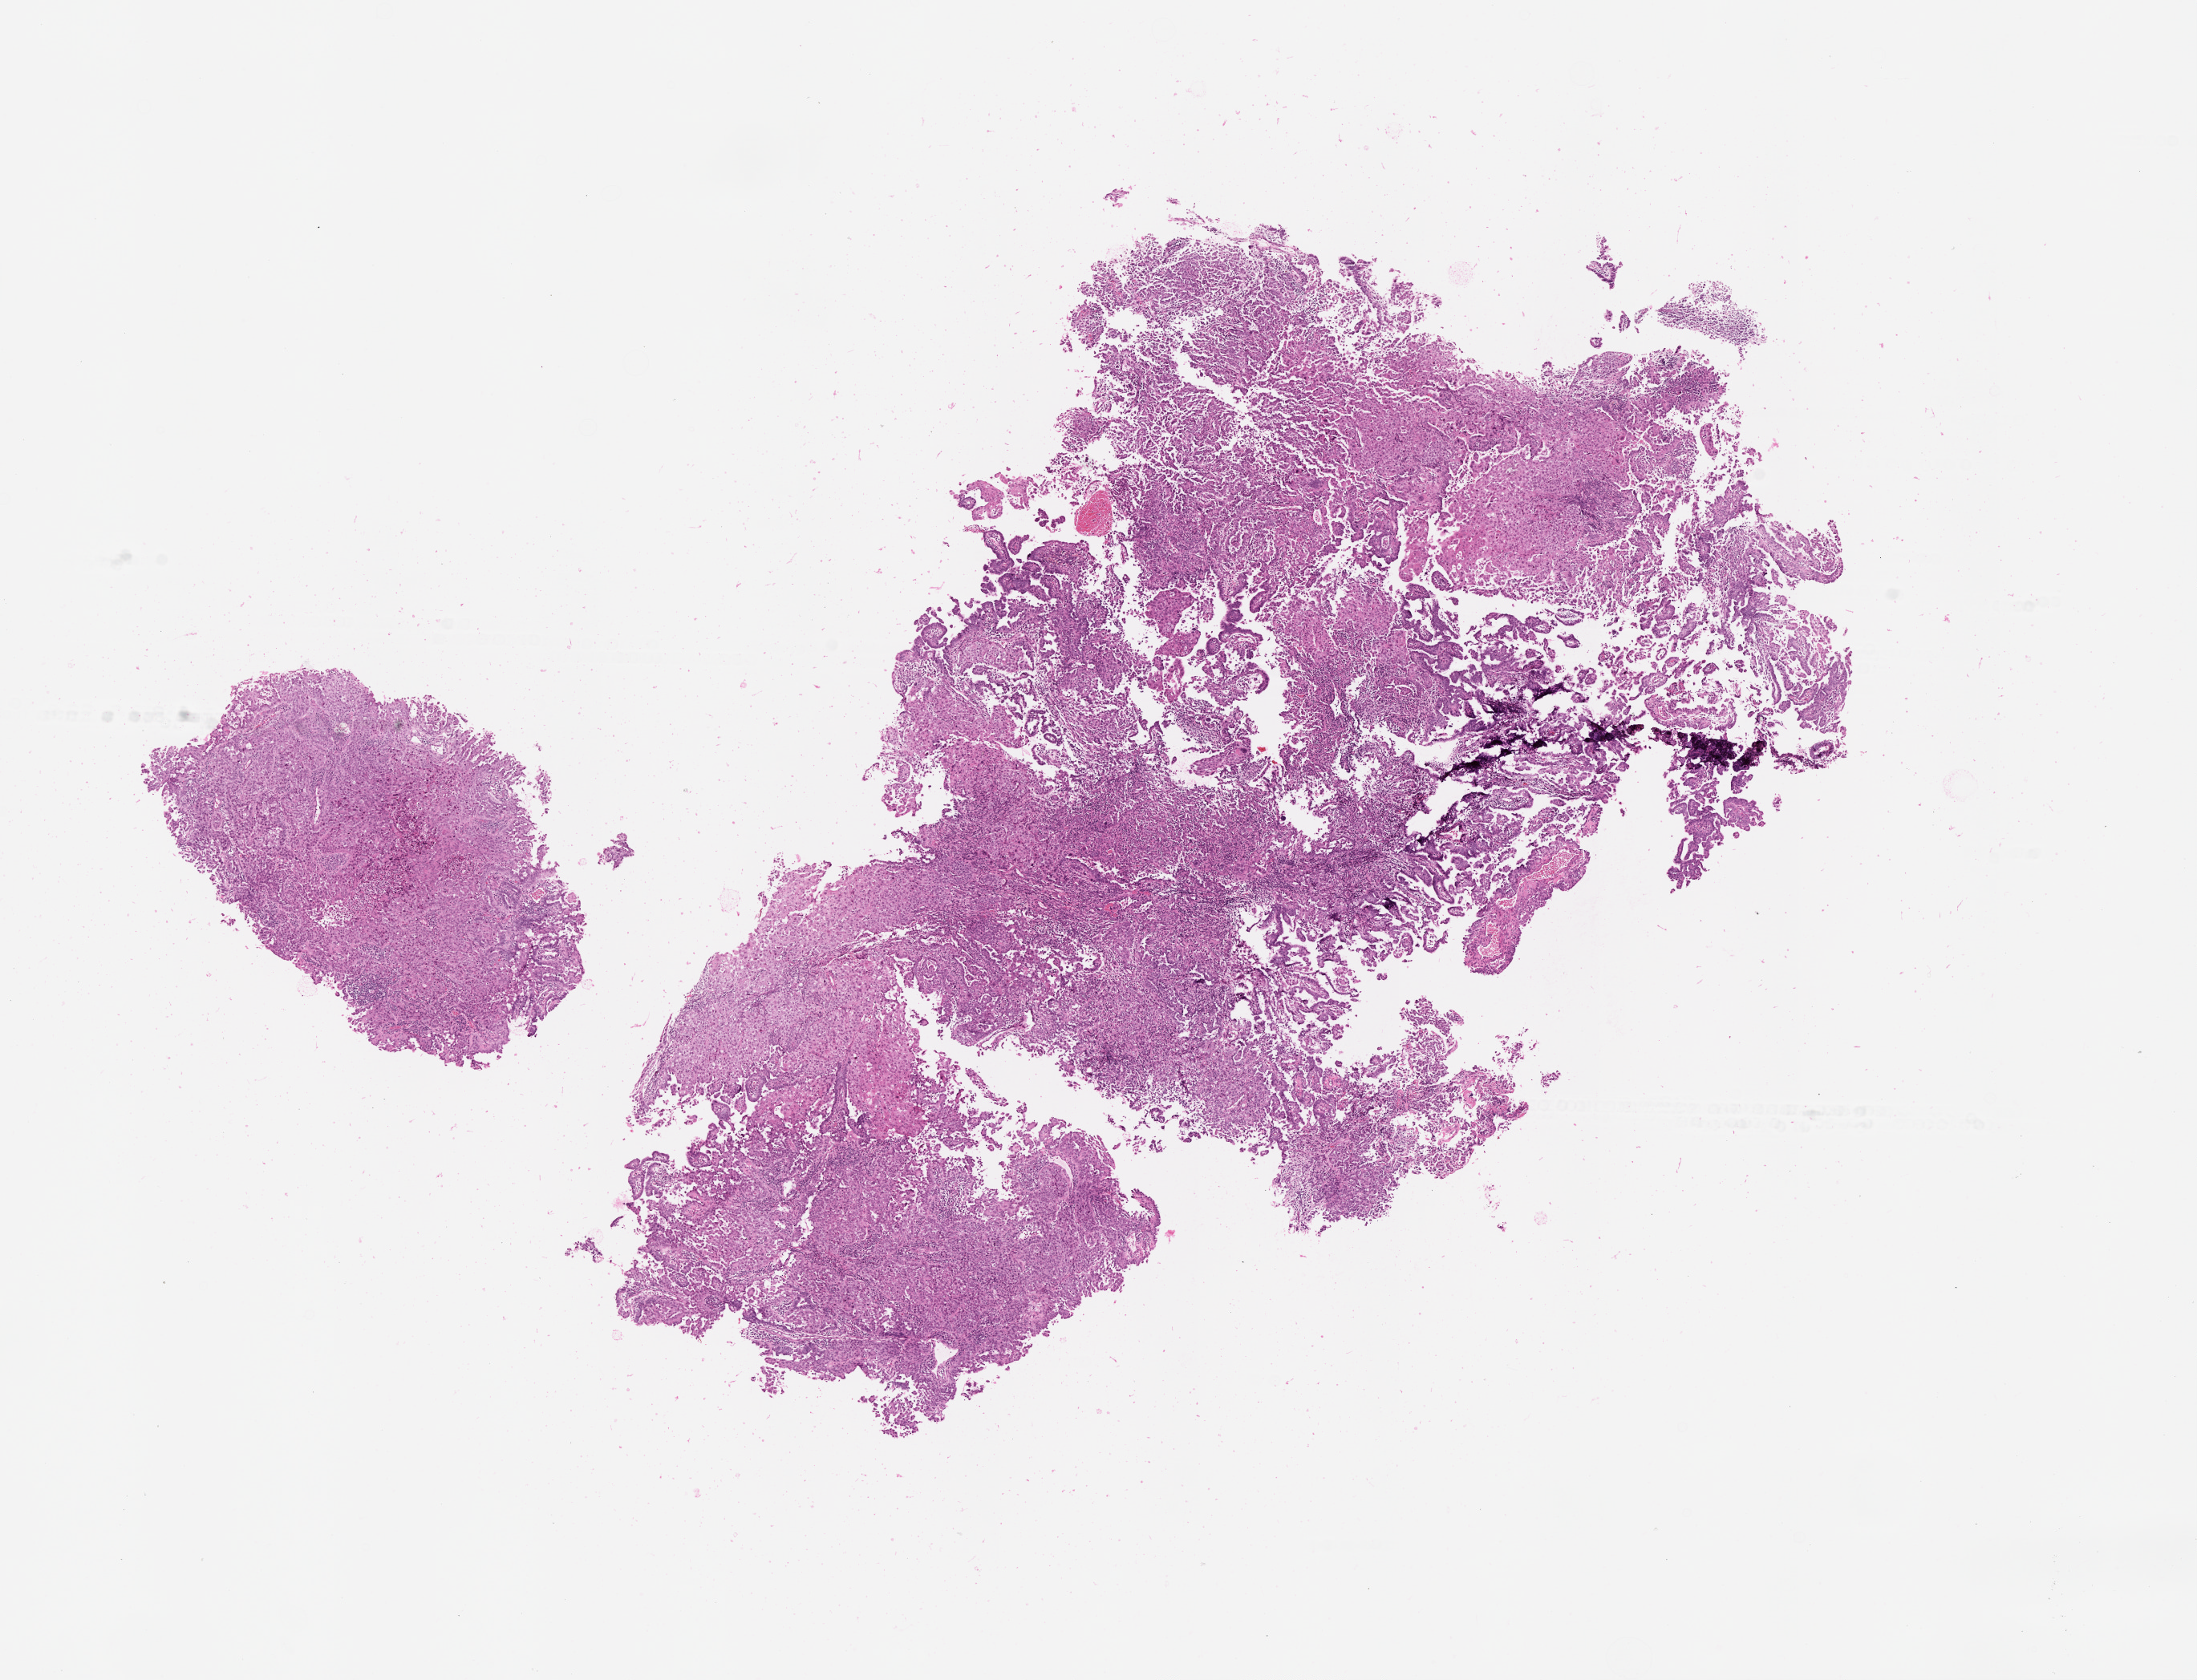
H&E-stained whole-slide image, whole scanned area (about 11.0 x 8.4 mm, from a 20x scan) shown as a low-resolution overview, tumour tissue sample, sampled site: uterus. 70-year-old female patient. Histologic grade: G3 (poorly differentiated). Slide review estimates, as recorded: tumour nuclei 80%, necrosis 0%.
AJCC pathologic stage: IVB. Diagnosis: Endometrioid adenocarcinoma, NOS.